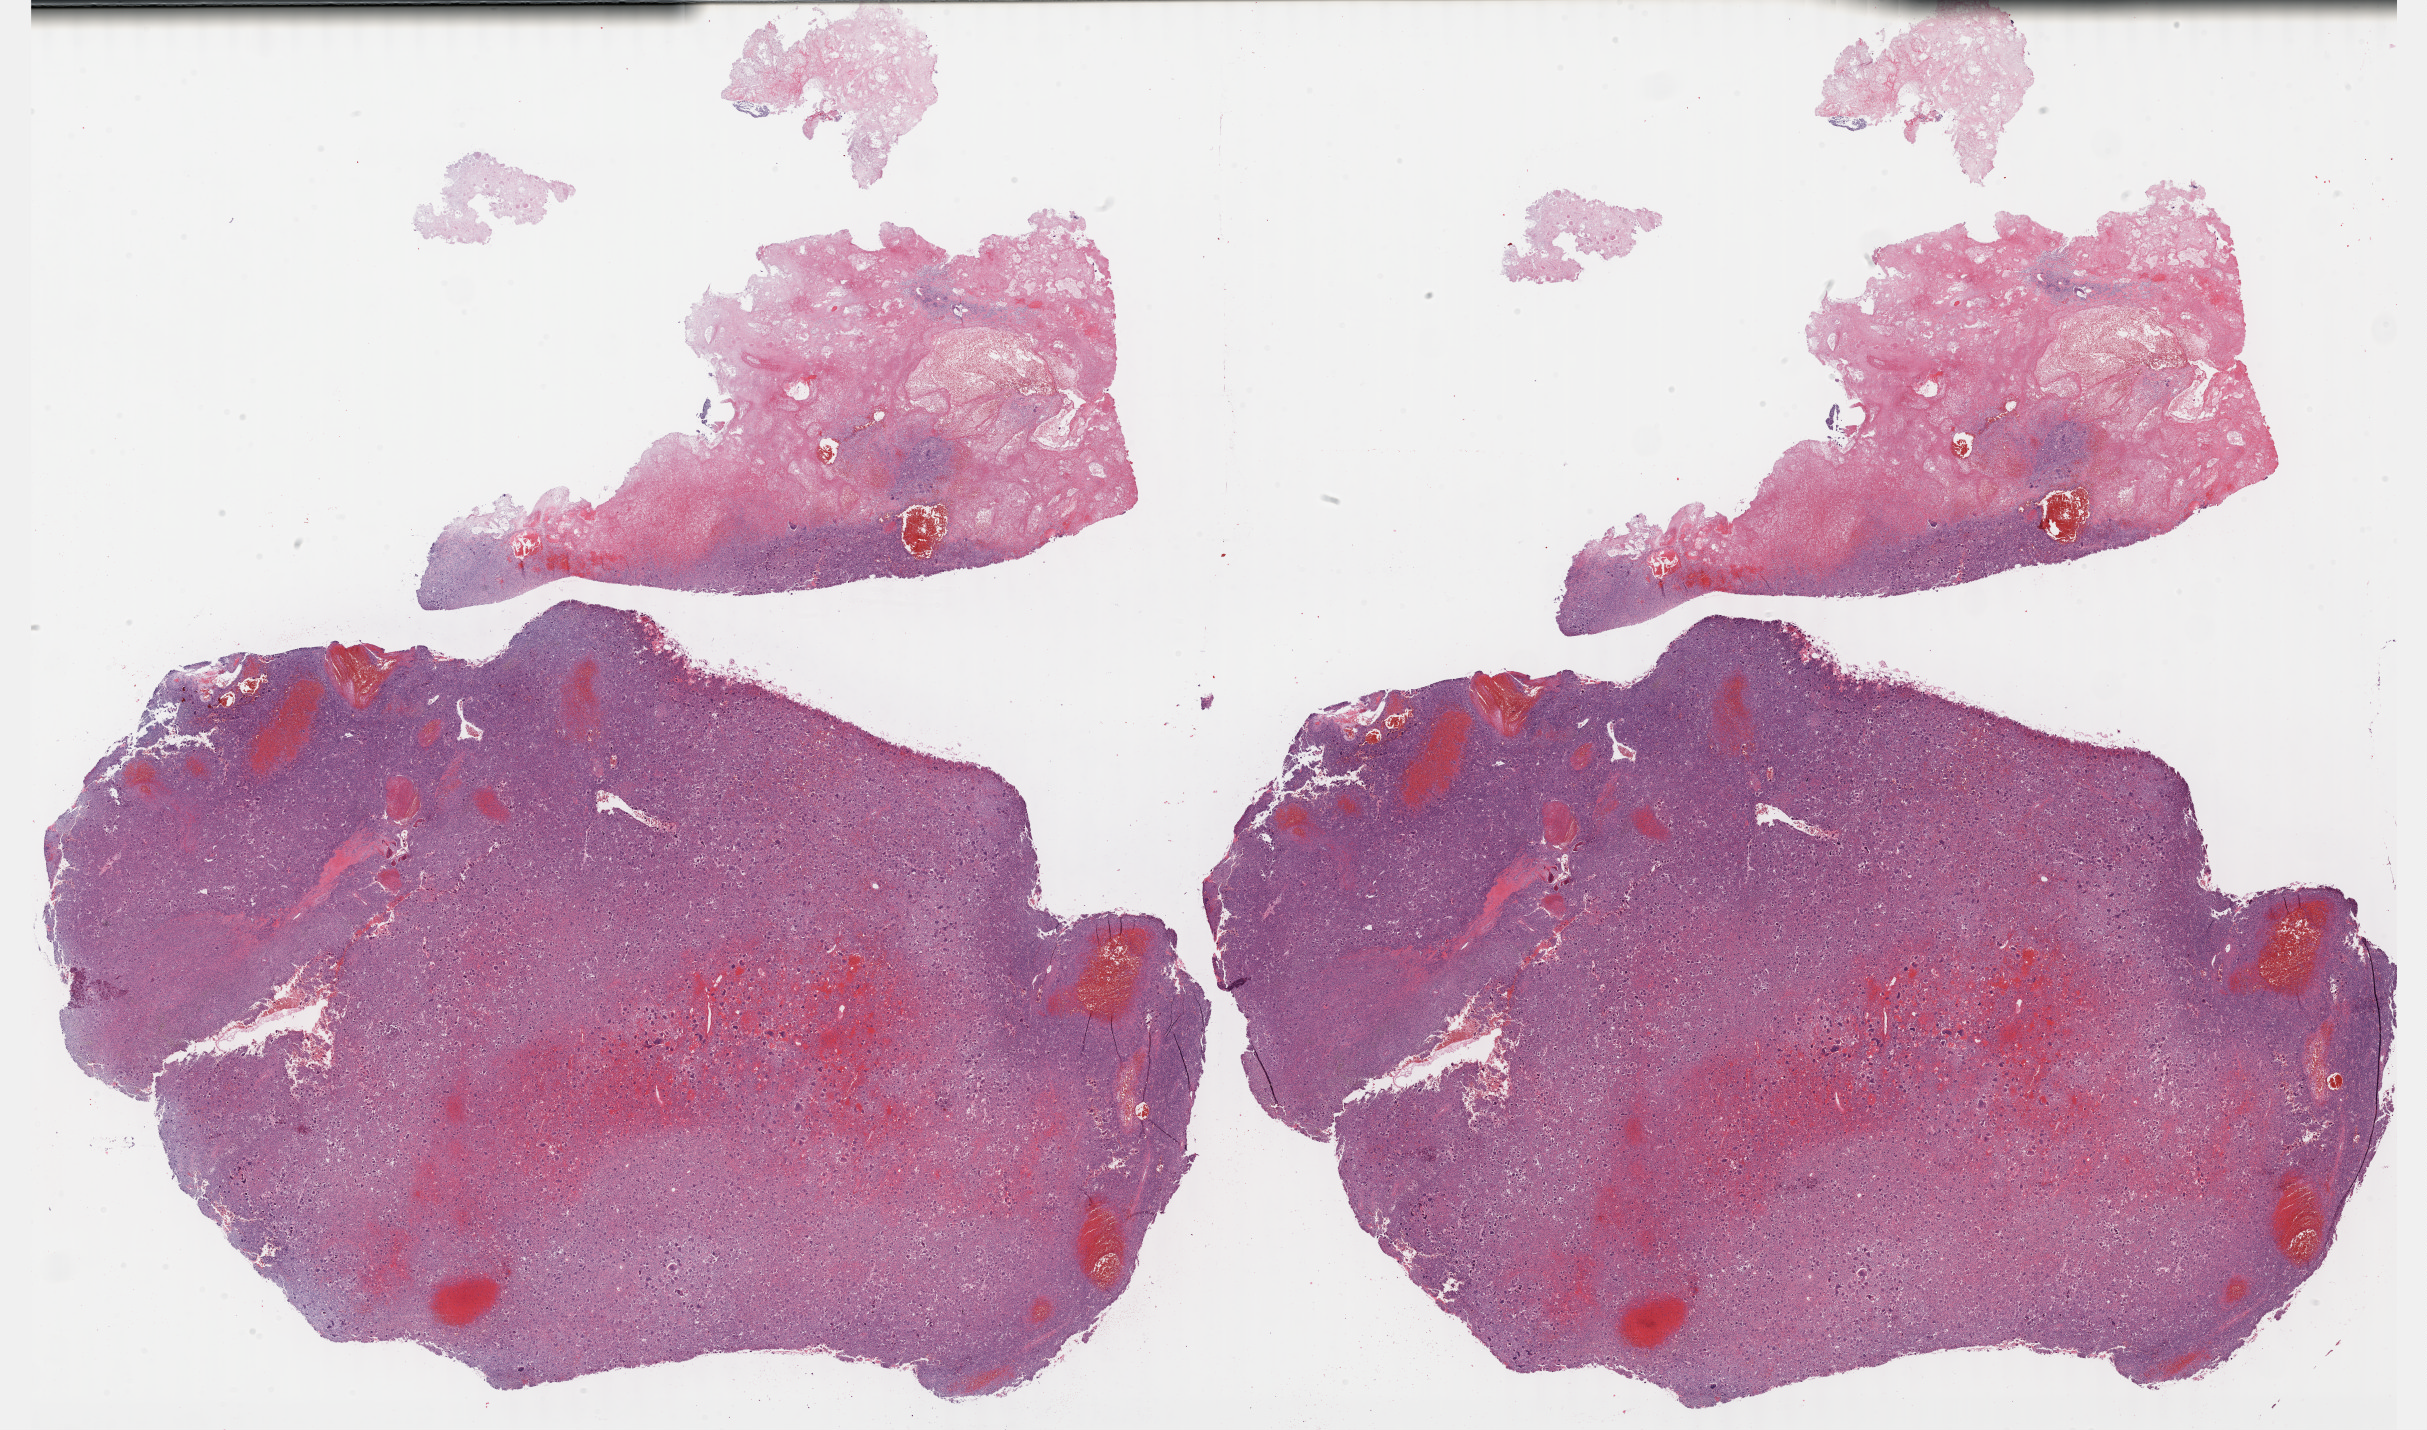
H&E whole-slide image, whole scanned area (about 39.2 x 23.1 mm, slide scanned at 40x) shown as a low-resolution overview; formalin-fixed paraffin-embedded (FFPE) diagnostic section; connective, subcutaneous and other soft tissues, primary tumour sample. Male, age 42 years at initial diagnosis.
- diagnosis: Malignant fibrous histiocytoma (connective, subcutaneous and other soft tissues of pelvis)